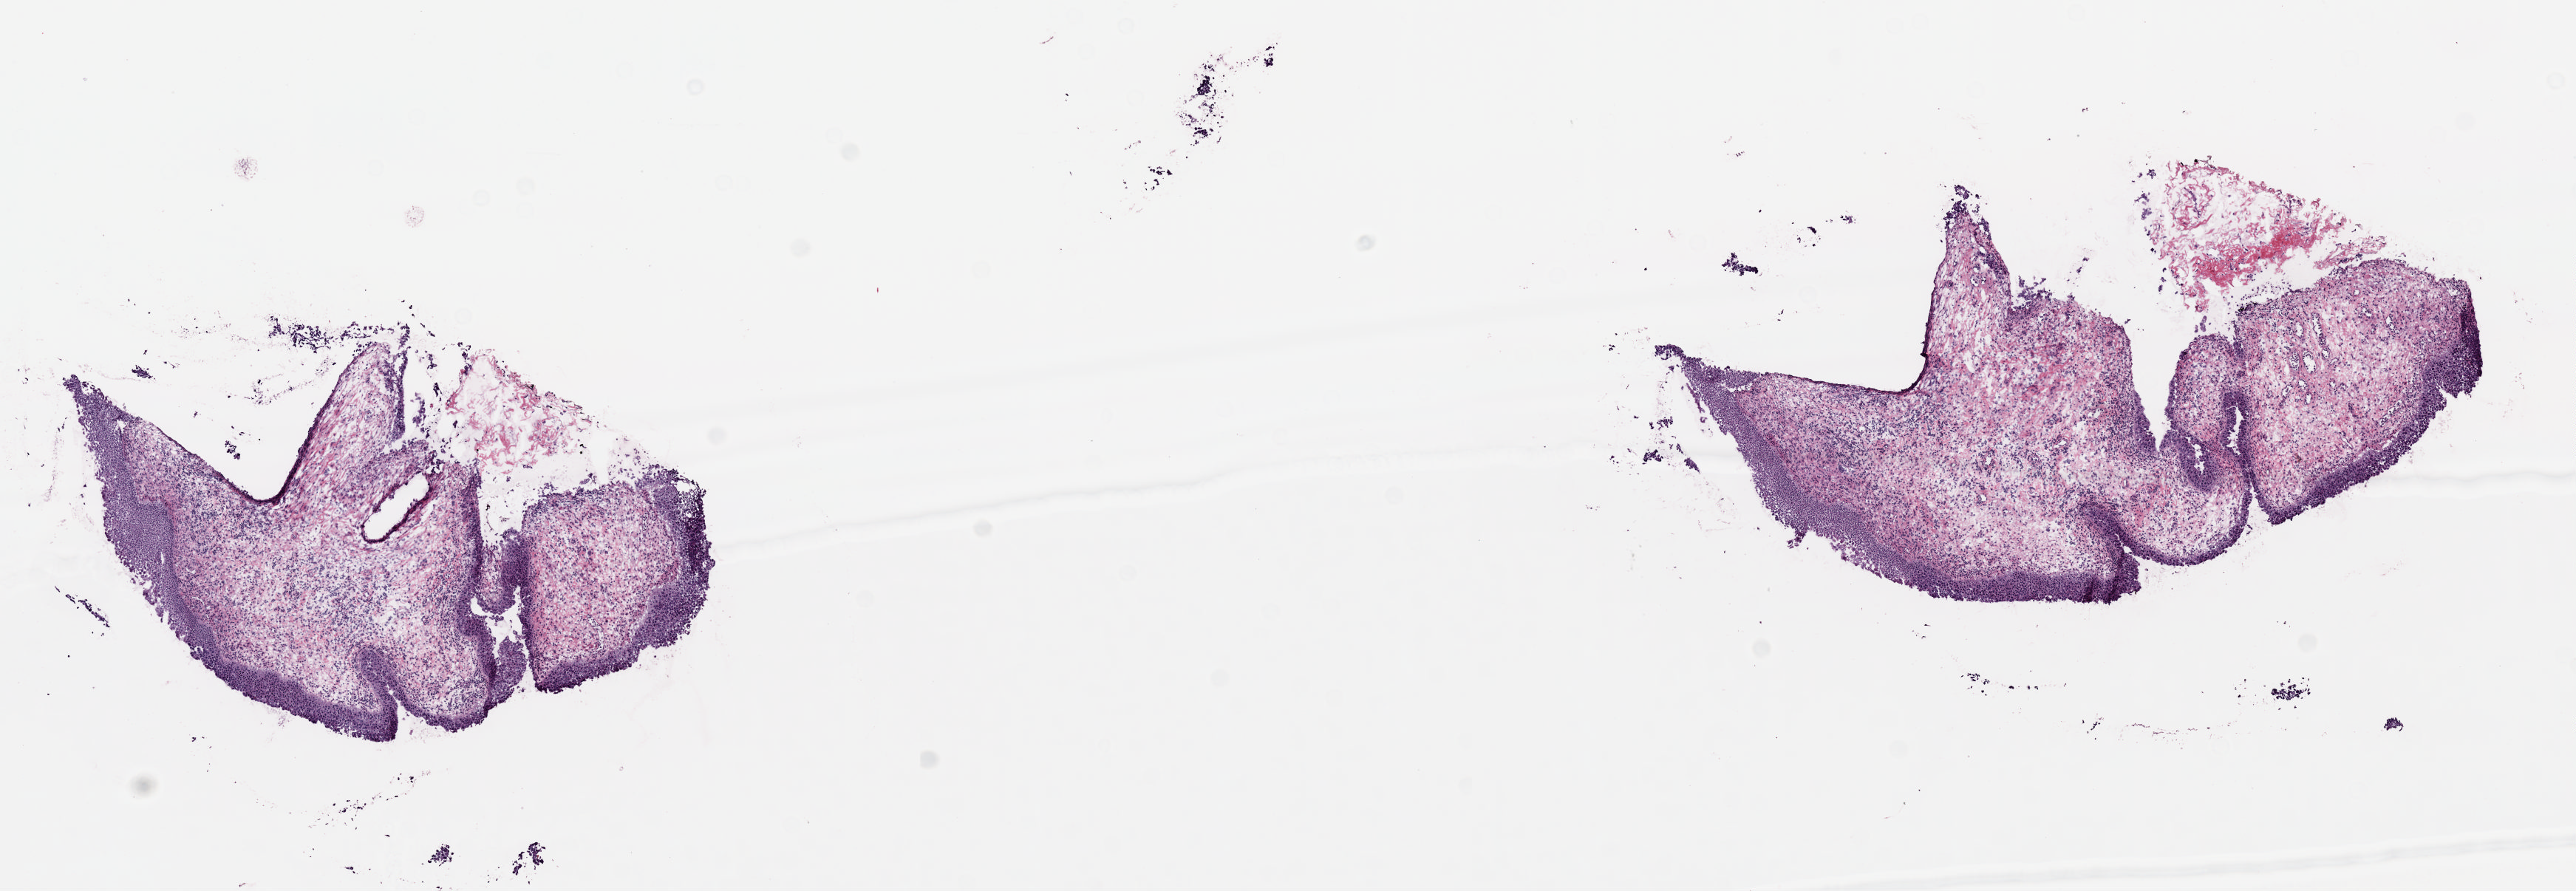
Digitized Hematoxylin and eosin (H&E) stained tissue section (whole slide) — low-resolution overview of the scanned area, about 13.8 x 4.8 mm (slide scanned at 20x). Frozen section from the top of the tissue portion. Bladder, solid tissue normal (non-tumour tissue) sample. Female patient; age at initial diagnosis 53 years. Slide review estimates, as recorded: tumour cells 0%, tumour nuclei 0%, normal cells 20%, stromal cells 80%, necrosis 0%. Infiltration values recorded for this section: lymphocyte infiltration 20%, monocyte infiltration 0%, neutrophil infiltration 1%.
This section: solid tissue normal (non-tumour) sample from the same patient. Patient diagnosis: Transitional cell carcinoma.